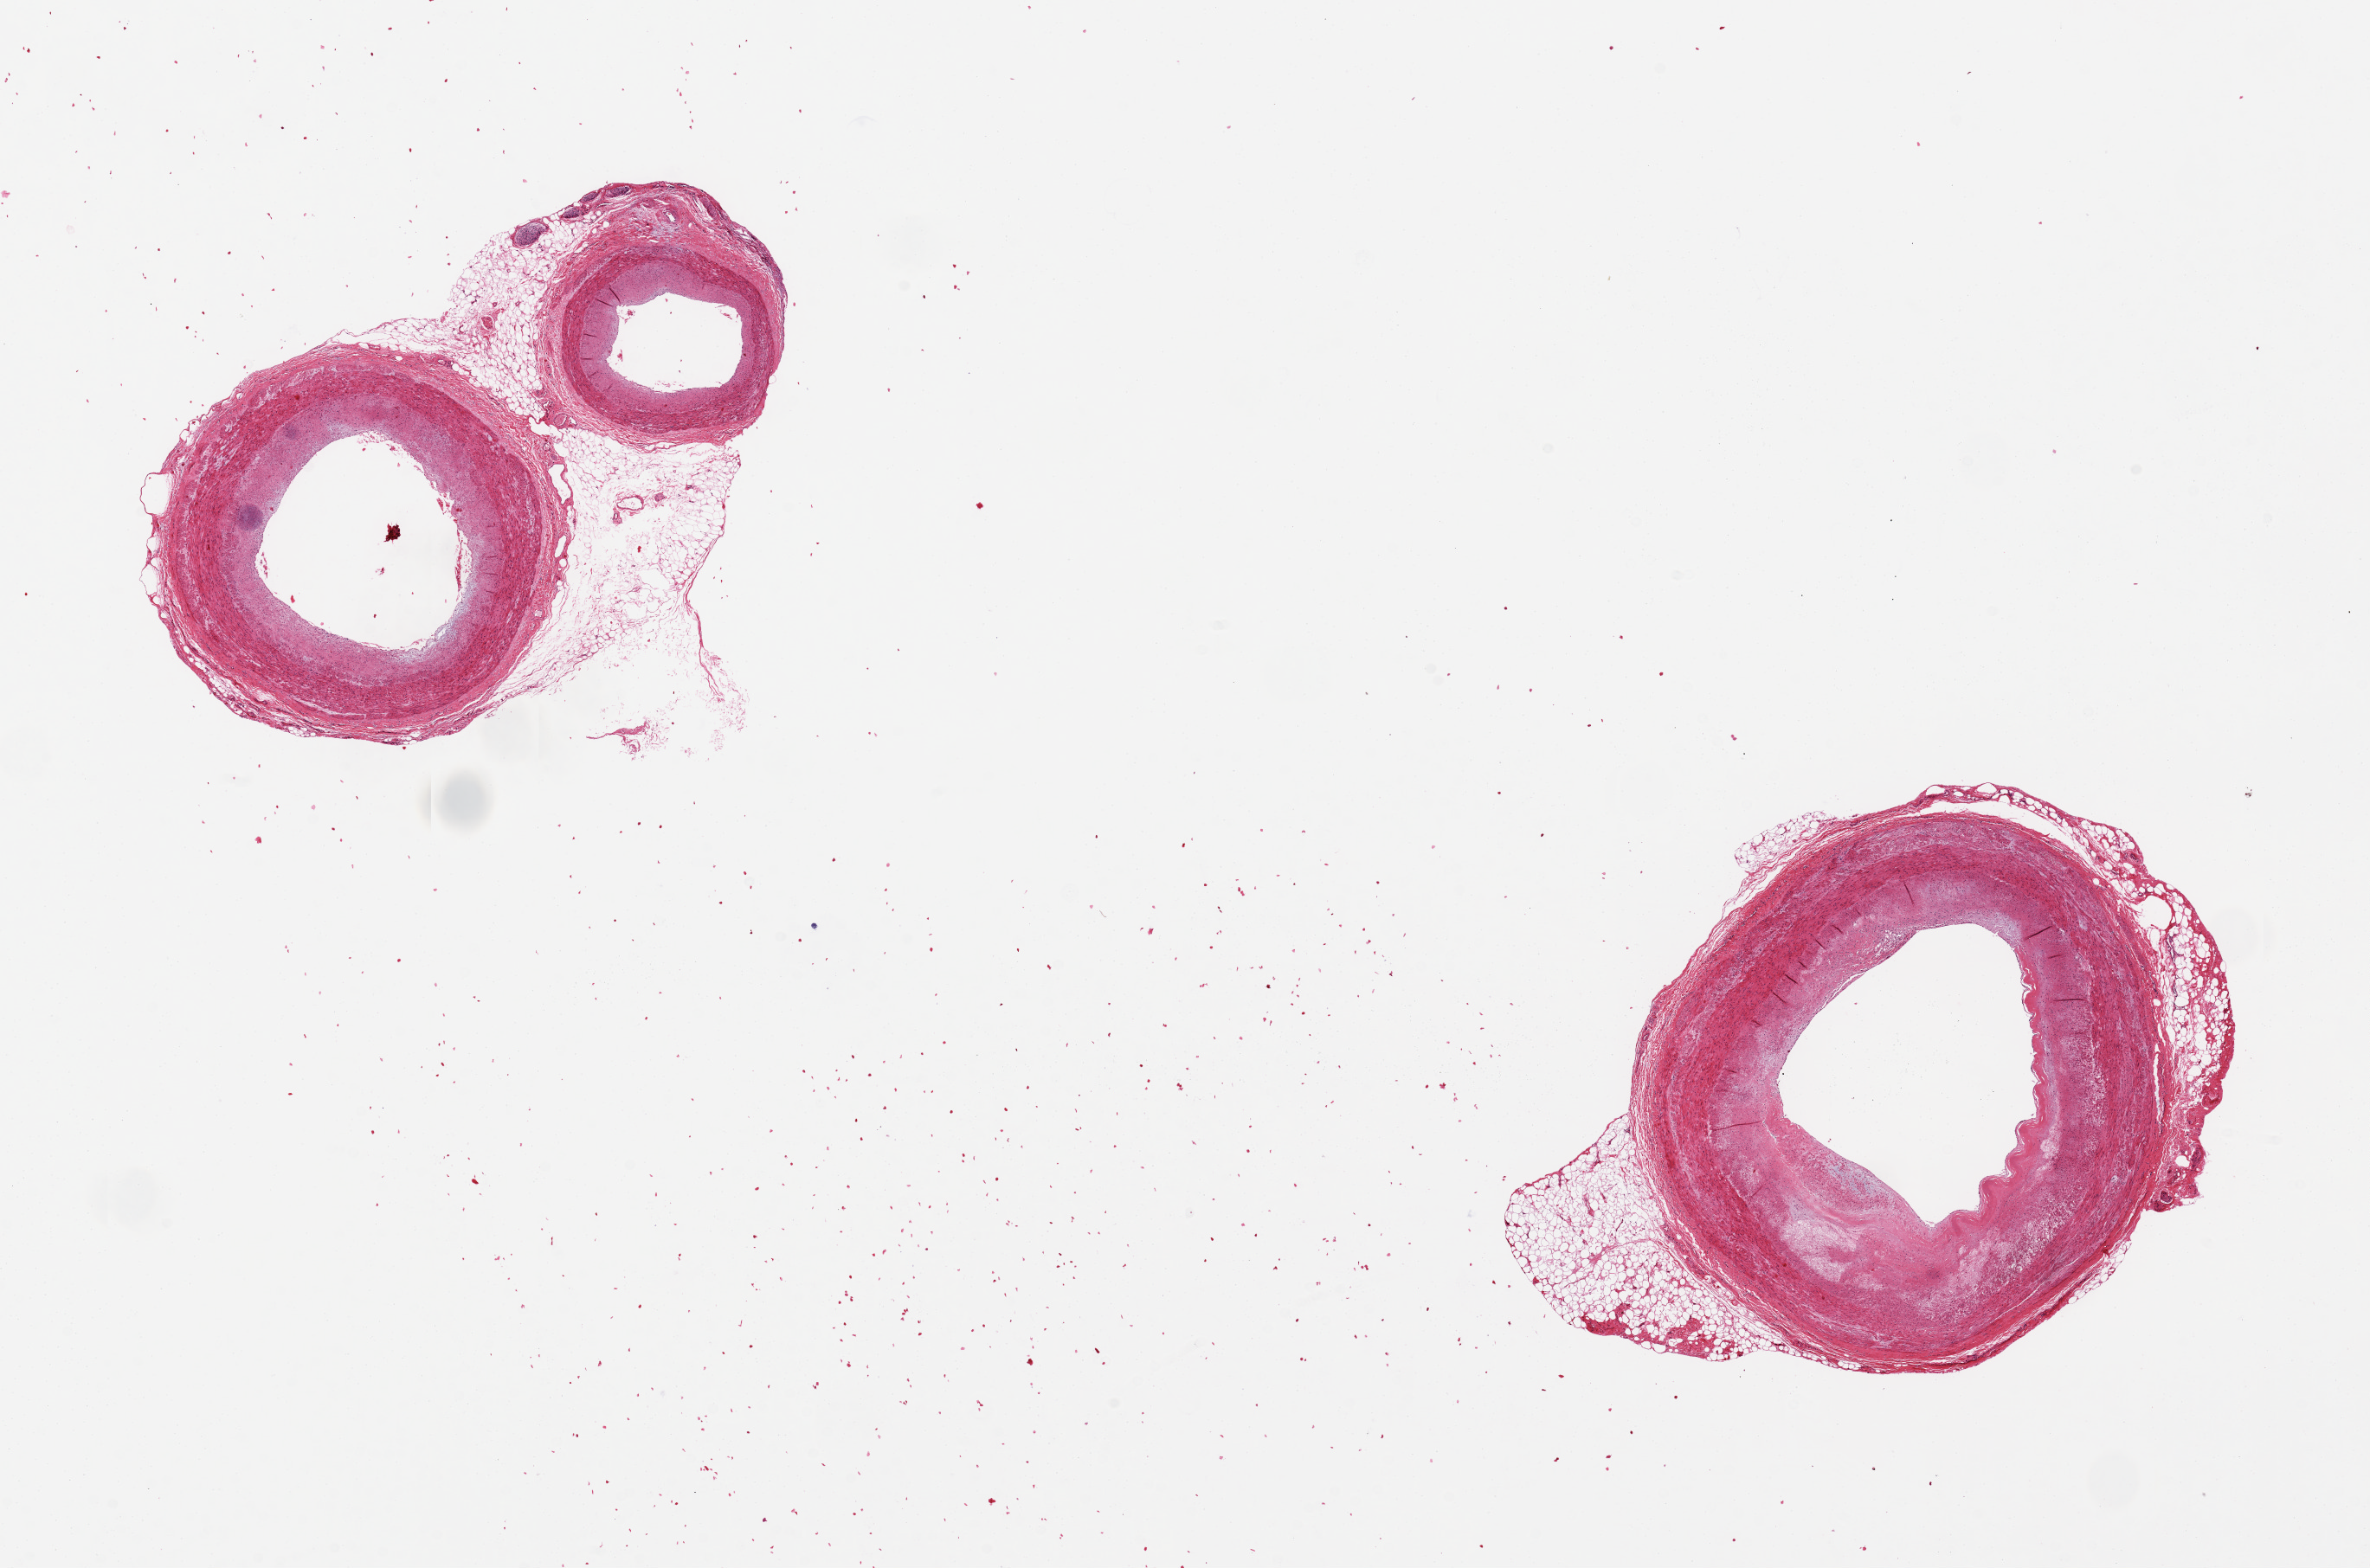
Haematoxylin and eosin whole-slide image, a low-resolution overview of the entire scanned area, about 21.7 x 14.3 mm. PAXgene-fixed paraffin-embedded (PFPE) section. Section of coronary artery (target tissue). Tissue donor sample. Male donor.
• review note (as recorded): 4.8 x 5.1mm specimen. ~20 circumferential atherosclerotic narrowing